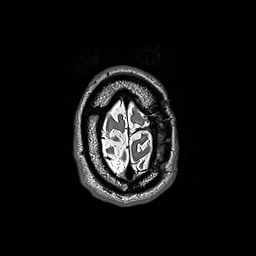
Brain MRI from a brain-tumour surgery series, one axial slice. Position 33 of 192 along the scan axis. 1 mm slice thickness. 256 × 256 image matrix. Case-level facts recorded for this patient, not image findings: histopathology: Oligodendroglioma; WHO grade: 3.
Structures marked on this image (expert manual segmentation):
- tumour: bounding box (x1, y1, x2, y2) in pixels: (138, 122, 142, 125)